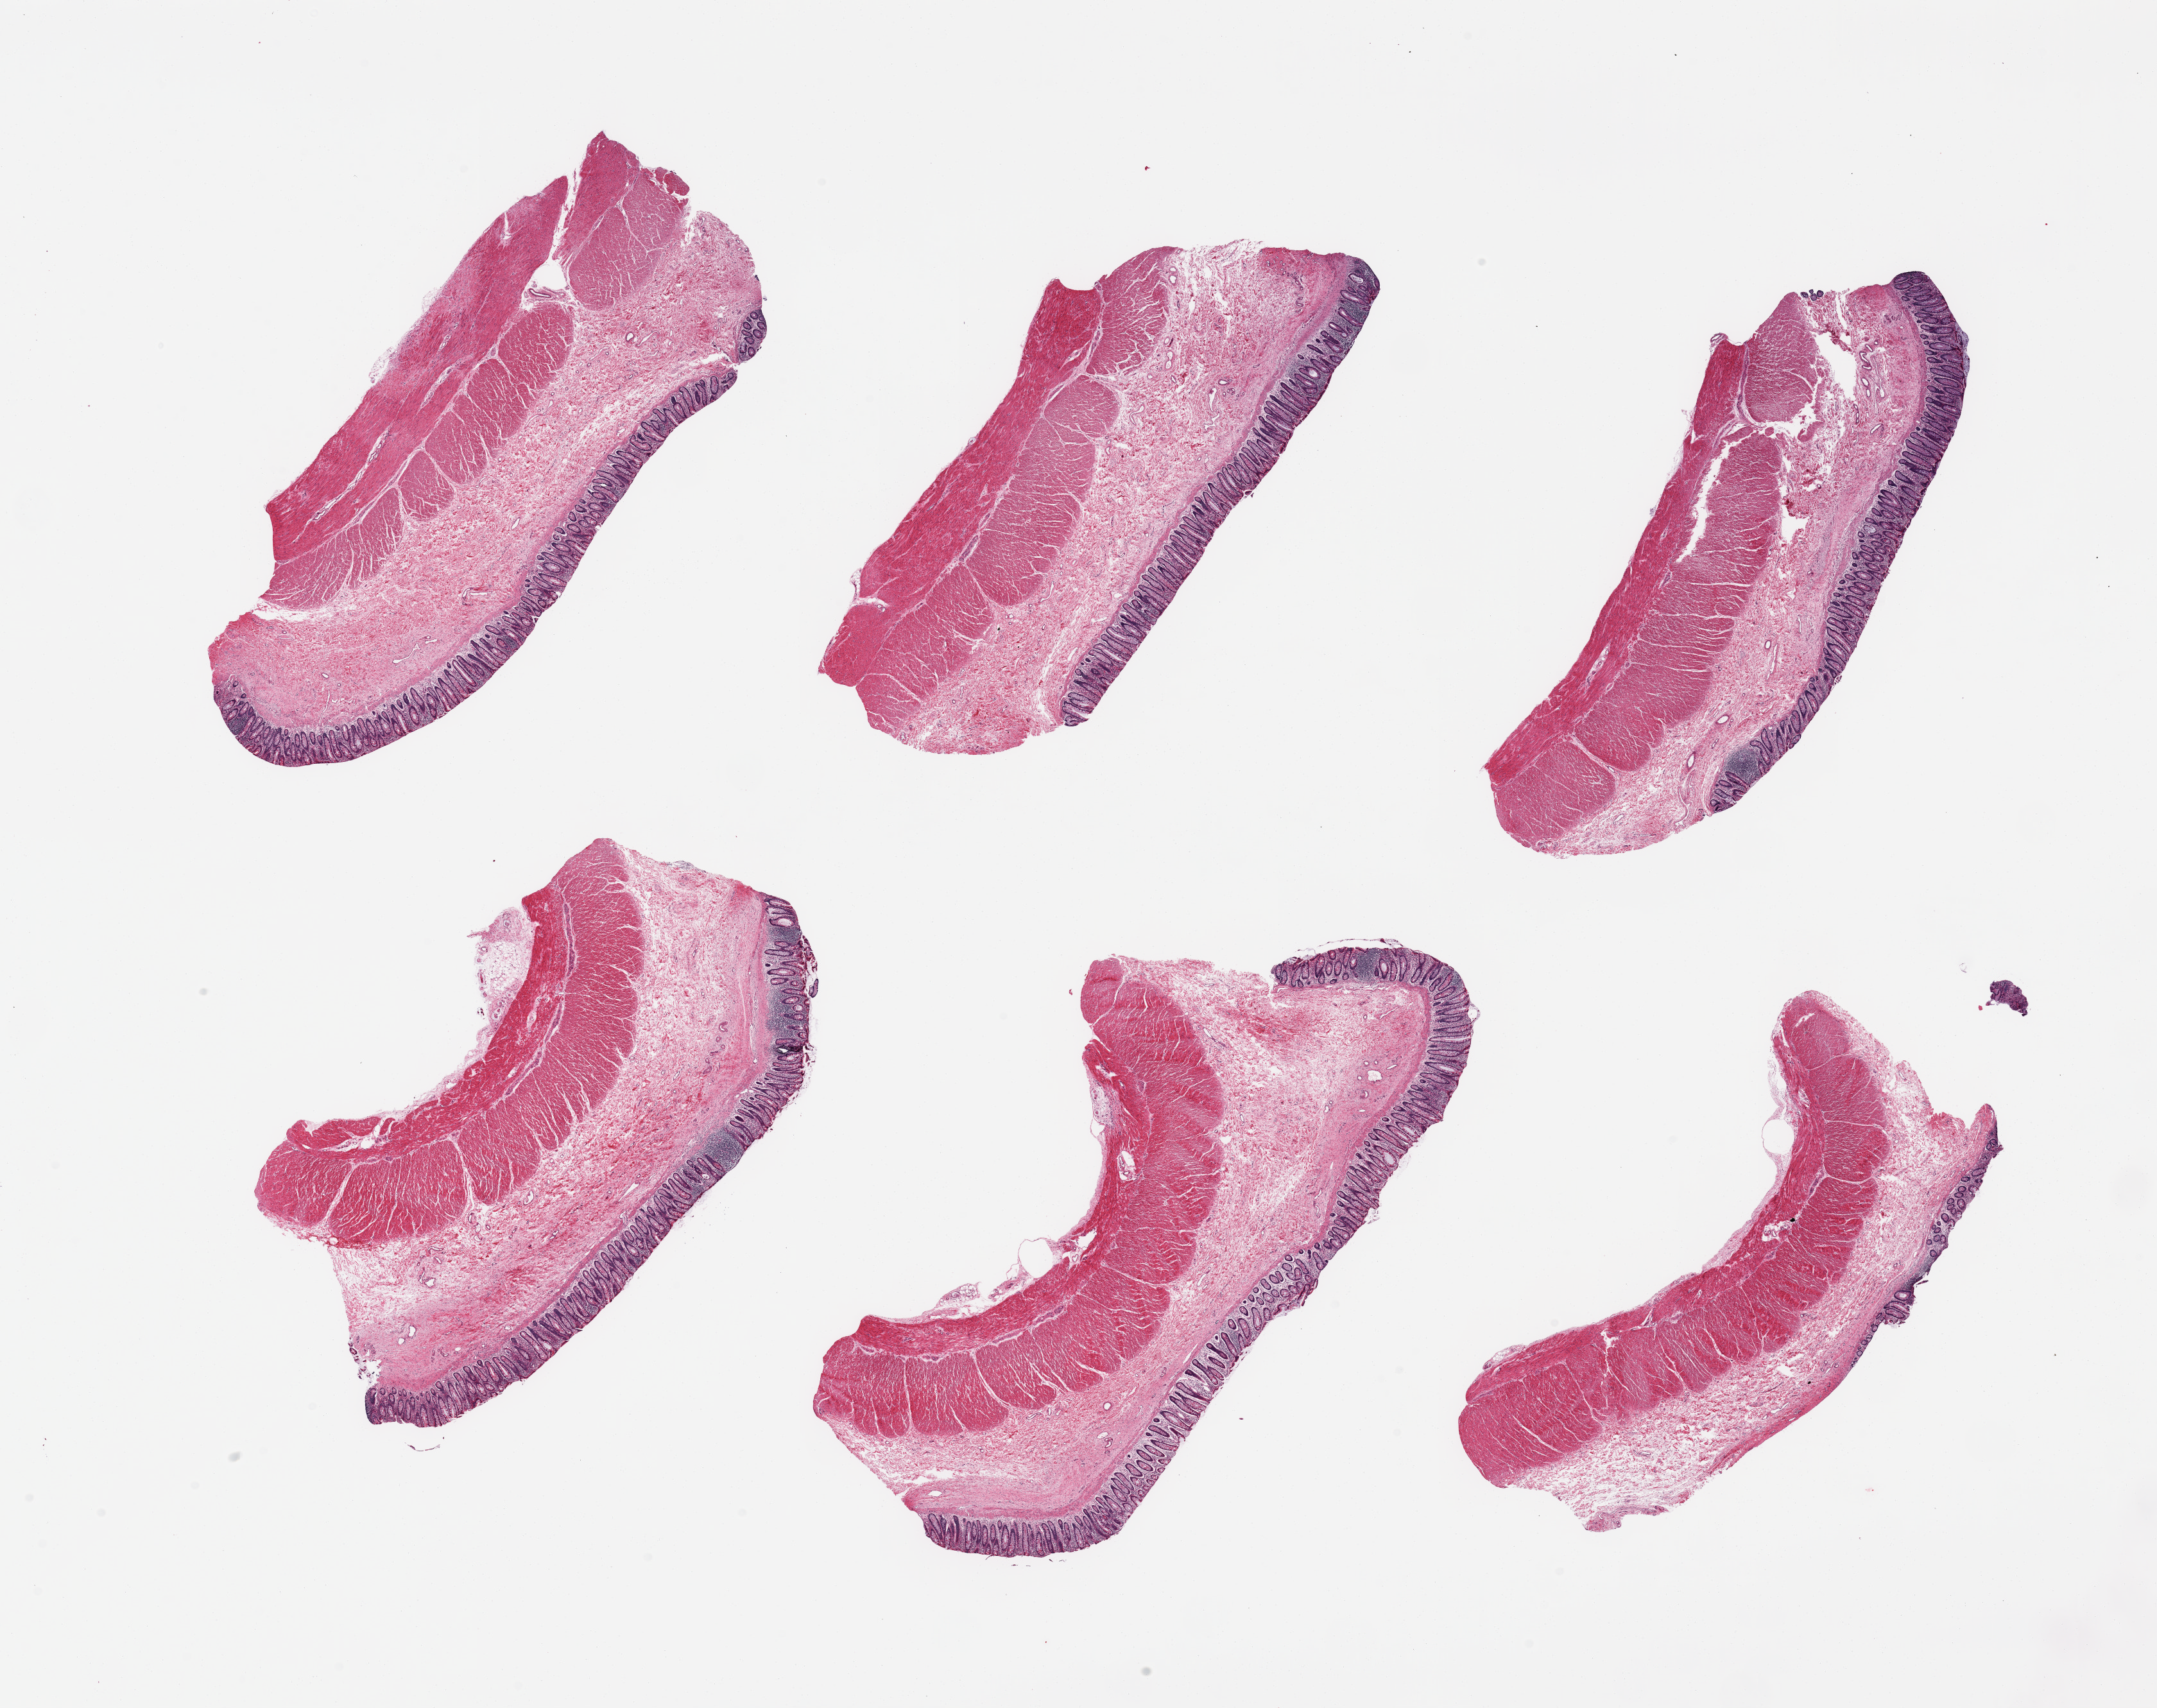
Hematoxylin and eosin (H&E) whole-slide image, shown as a low-resolution overview of the whole scanned area (about 26.6 x 21.0 mm, acquisition: 20x scan). PAXgene-fixed paraffin-embedded (PFPE) section. Sampled site (target tissue): transverse colon. Donor tissue sample. Female donor.
Review note (as recorded): 6 pieces; mucosa and muscularis.